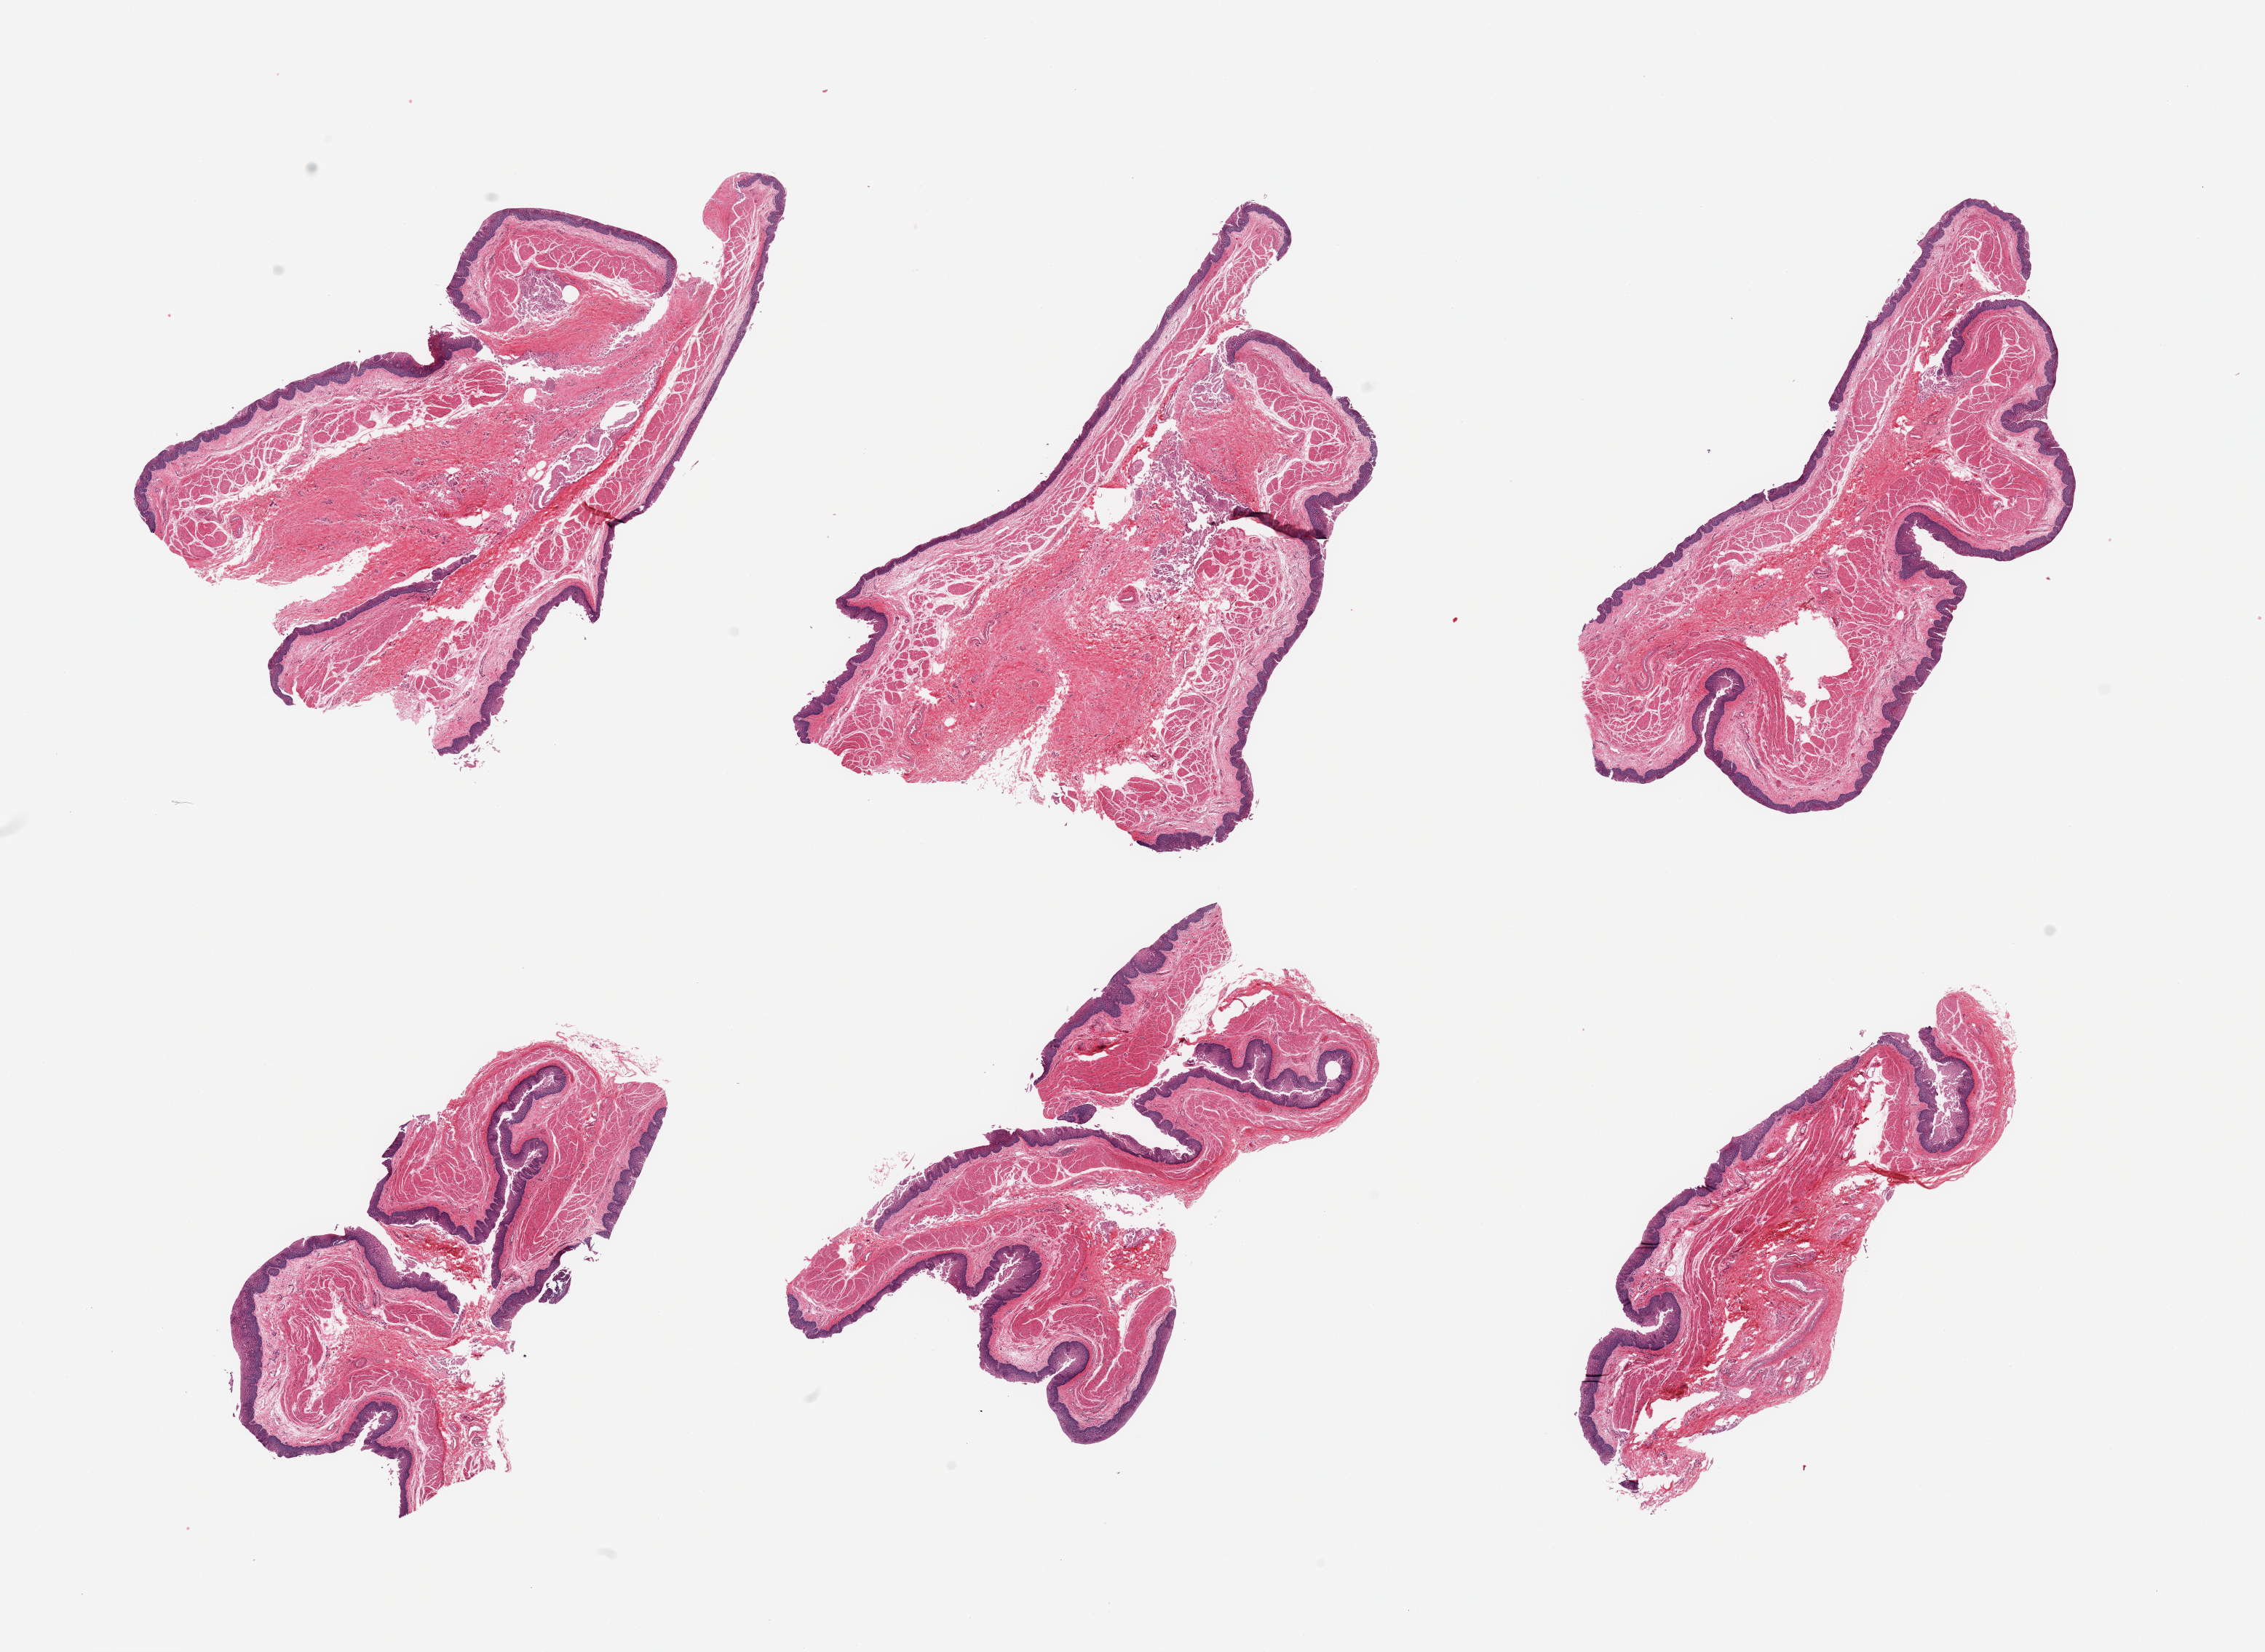
Whole-slide image, haematoxylin and eosin stain, low-resolution overview of the scanned area, about 24.6 x 18.0 mm. PAXgene-fixed, paraffin-embedded tissue. Target tissue: esophageal mucous membrane. Donor tissue sample.
Review note (as recorded): 6 pieces, squamous mucosa up to ~0.2mm, 10-15% thickness.